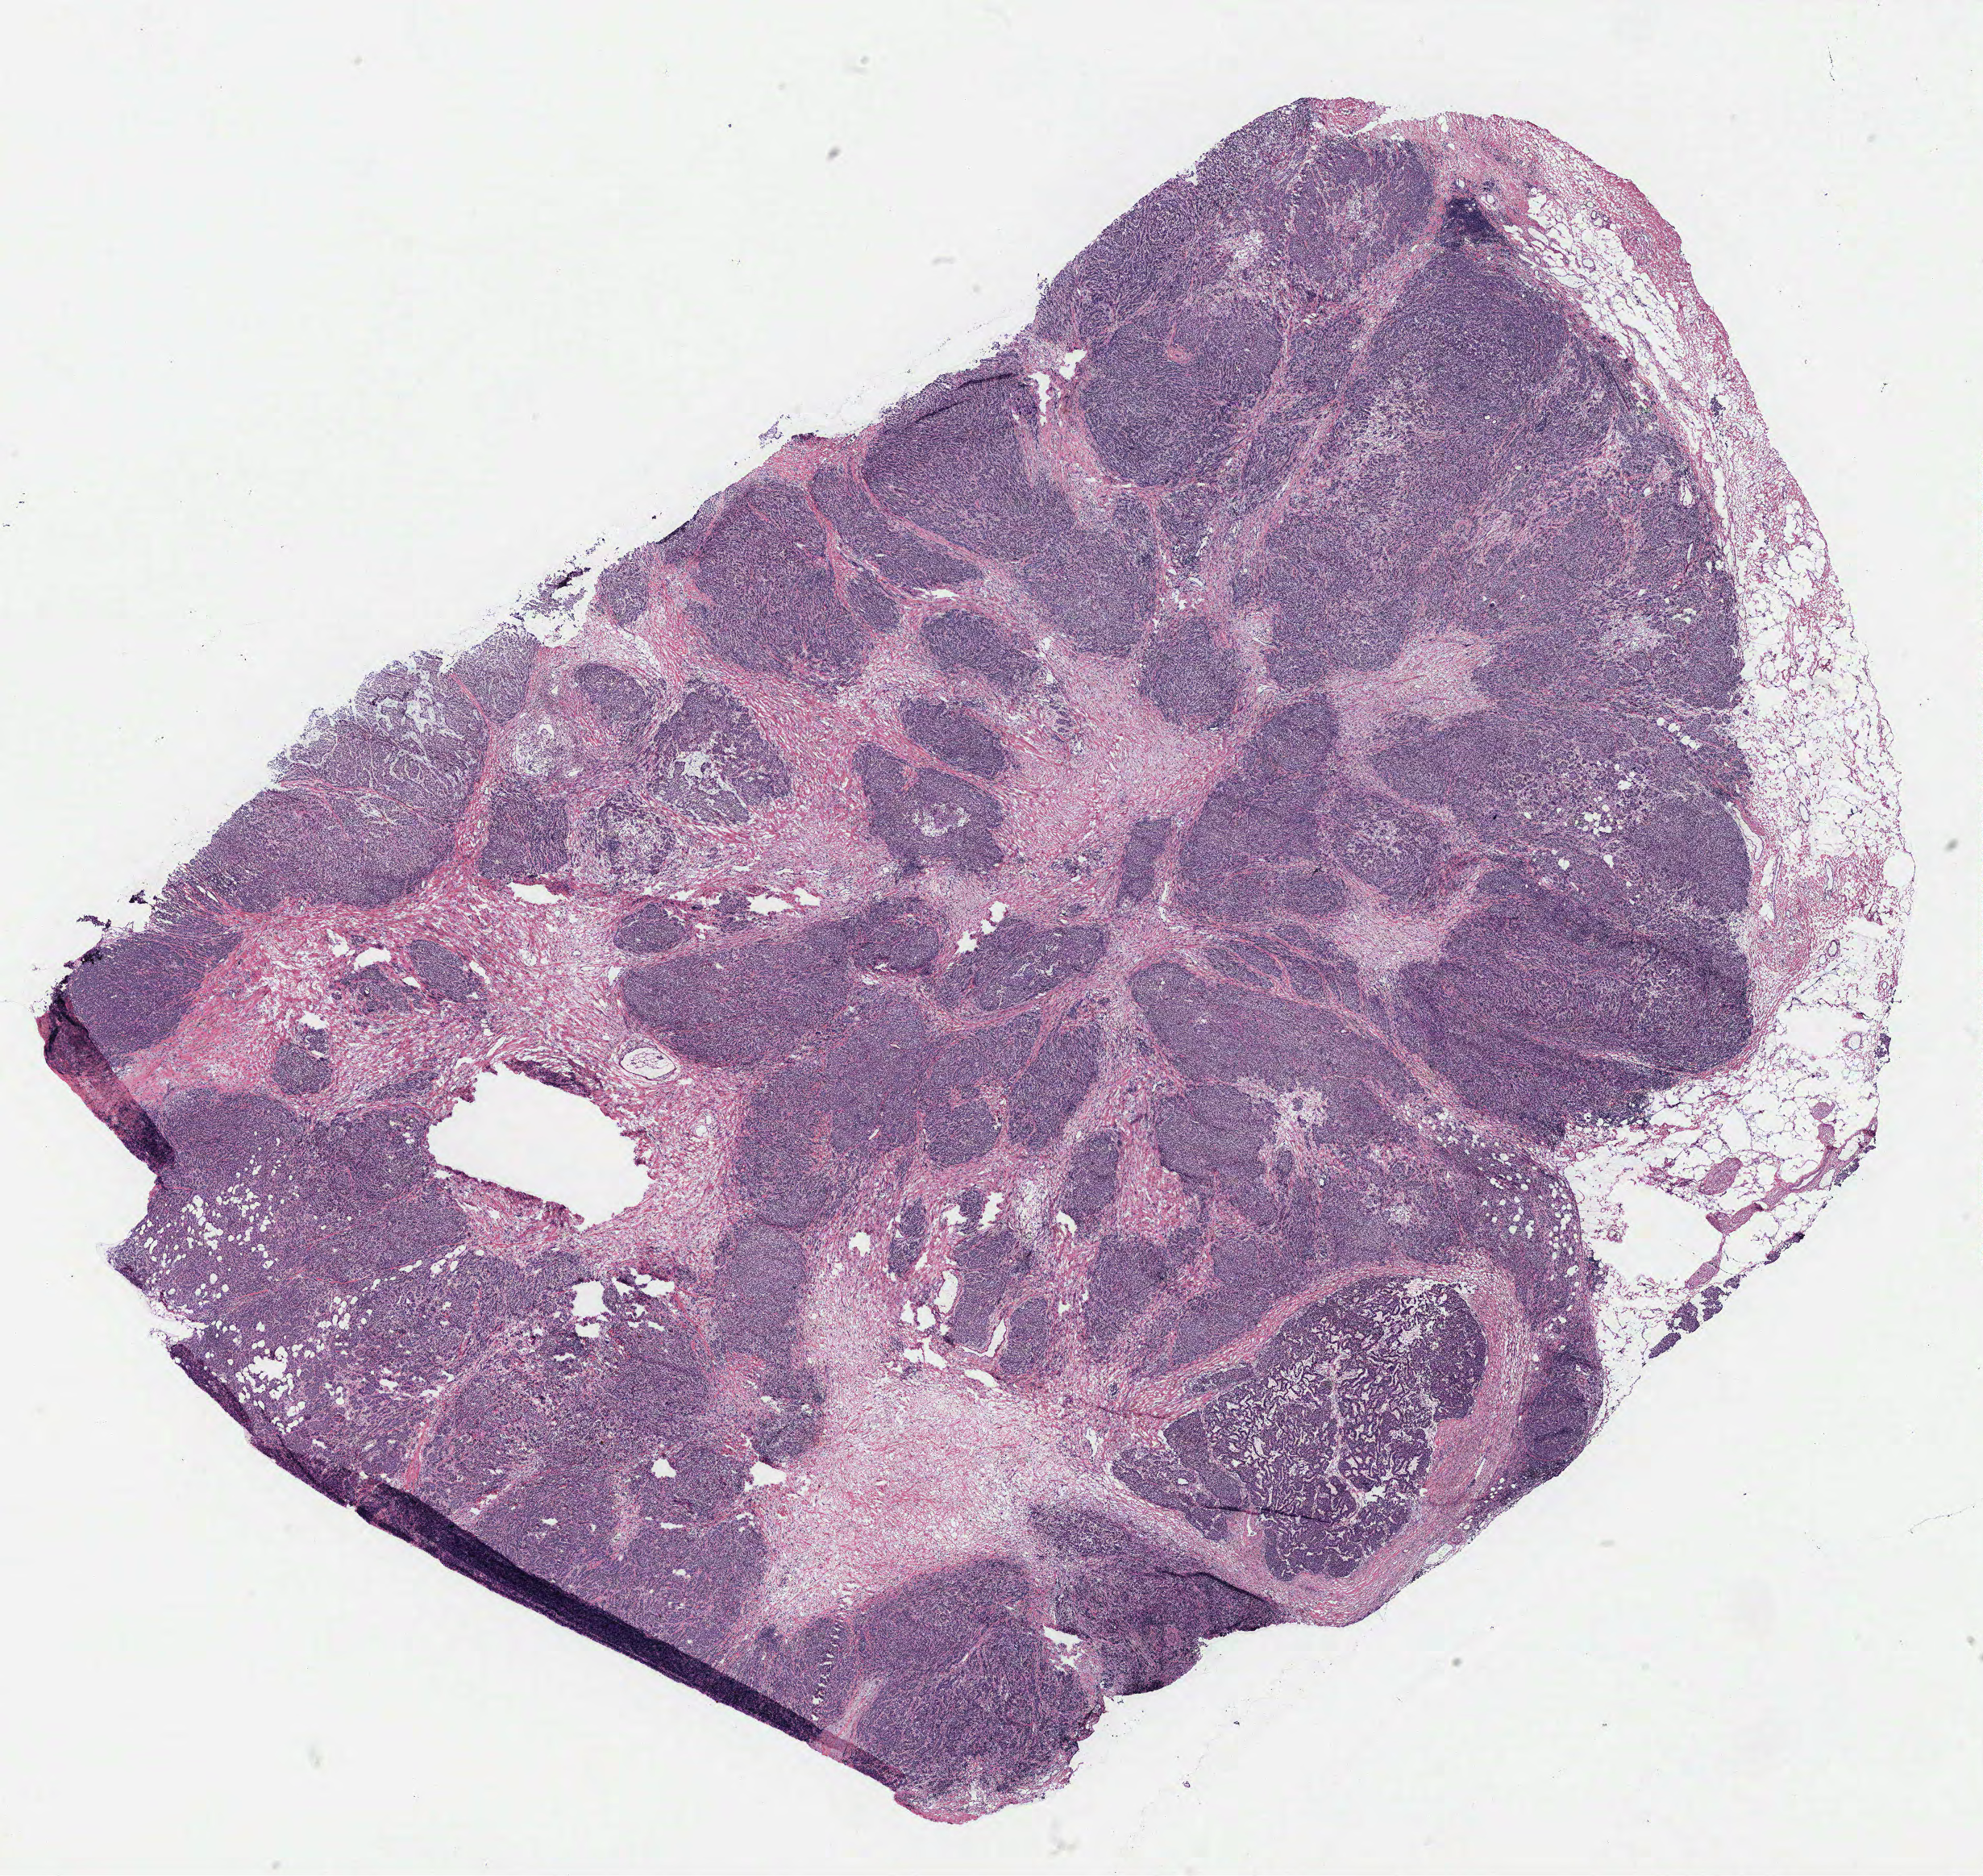
Whole-slide histology image, H&E-stained — a low-resolution overview of the entire scanned area, about 19.7 x 18.6 mm, tumour tissue sample, breast. Patient: female, age 76 years.
AJCC pathologic stage: IIA. Diagnosis: Infiltrating duct carcinoma, NOS.